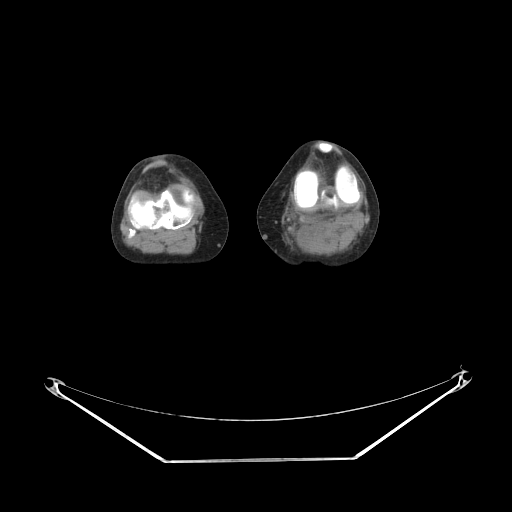
CT of an extremity soft-tissue mass (from a PET/CT study), one axial slice; reconstruction kernel STANDARD; soft-tissue window (W 400 / L 40 HU); 512 × 512 image matrix, field of view 500 × 500 mm. Female patient. From the clinical record (not read from this slice): histological type: extraskeletal high grade osteogenic sarcoma; grade: high; site of the primary tumour: left calf.
Outlined on this slice (expert contour drawn on MRI and transferred to this co-registered scan by the dataset authors):
- gross tumour volume (mass): bounding box <301,231,312,243> (left, top, right, bottom; pixels)